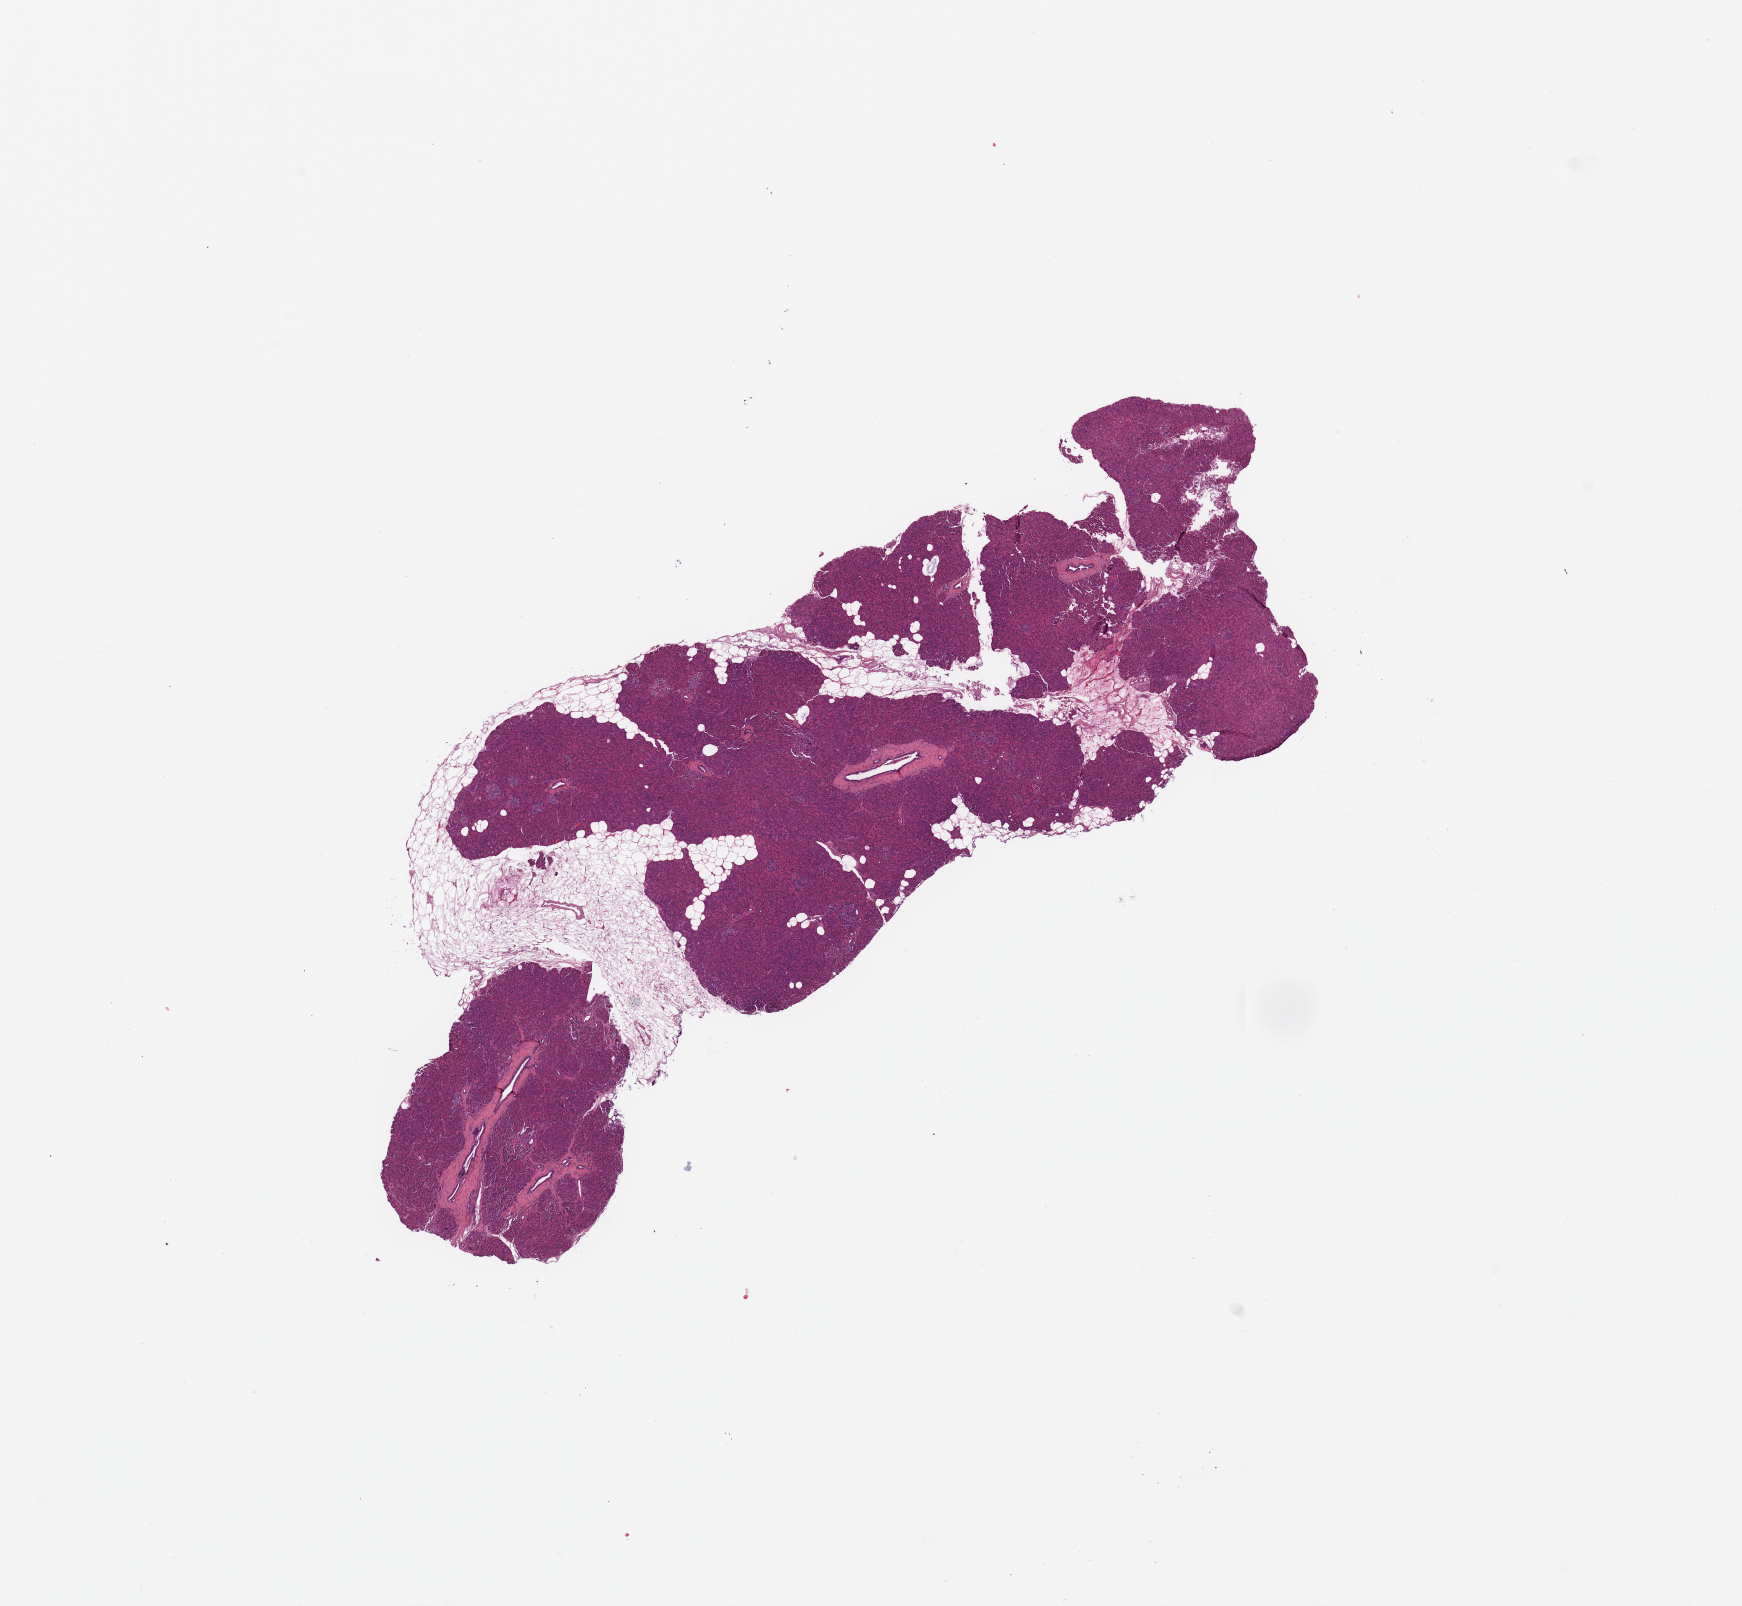
Whole-slide histology image, Hematoxylin and eosin (H&E) stained, whole scanned area (about 13.8 x 12.7 mm, from a 20x scan) shown as a low-resolution overview. Normal (non-tumour) tissue sample, sampled site: pancreas. Patient: male, age 80 years.
- this section: normal (non-tumour) tissue from the same patient
- patient diagnosis: Infiltrating duct carcinoma, NOS